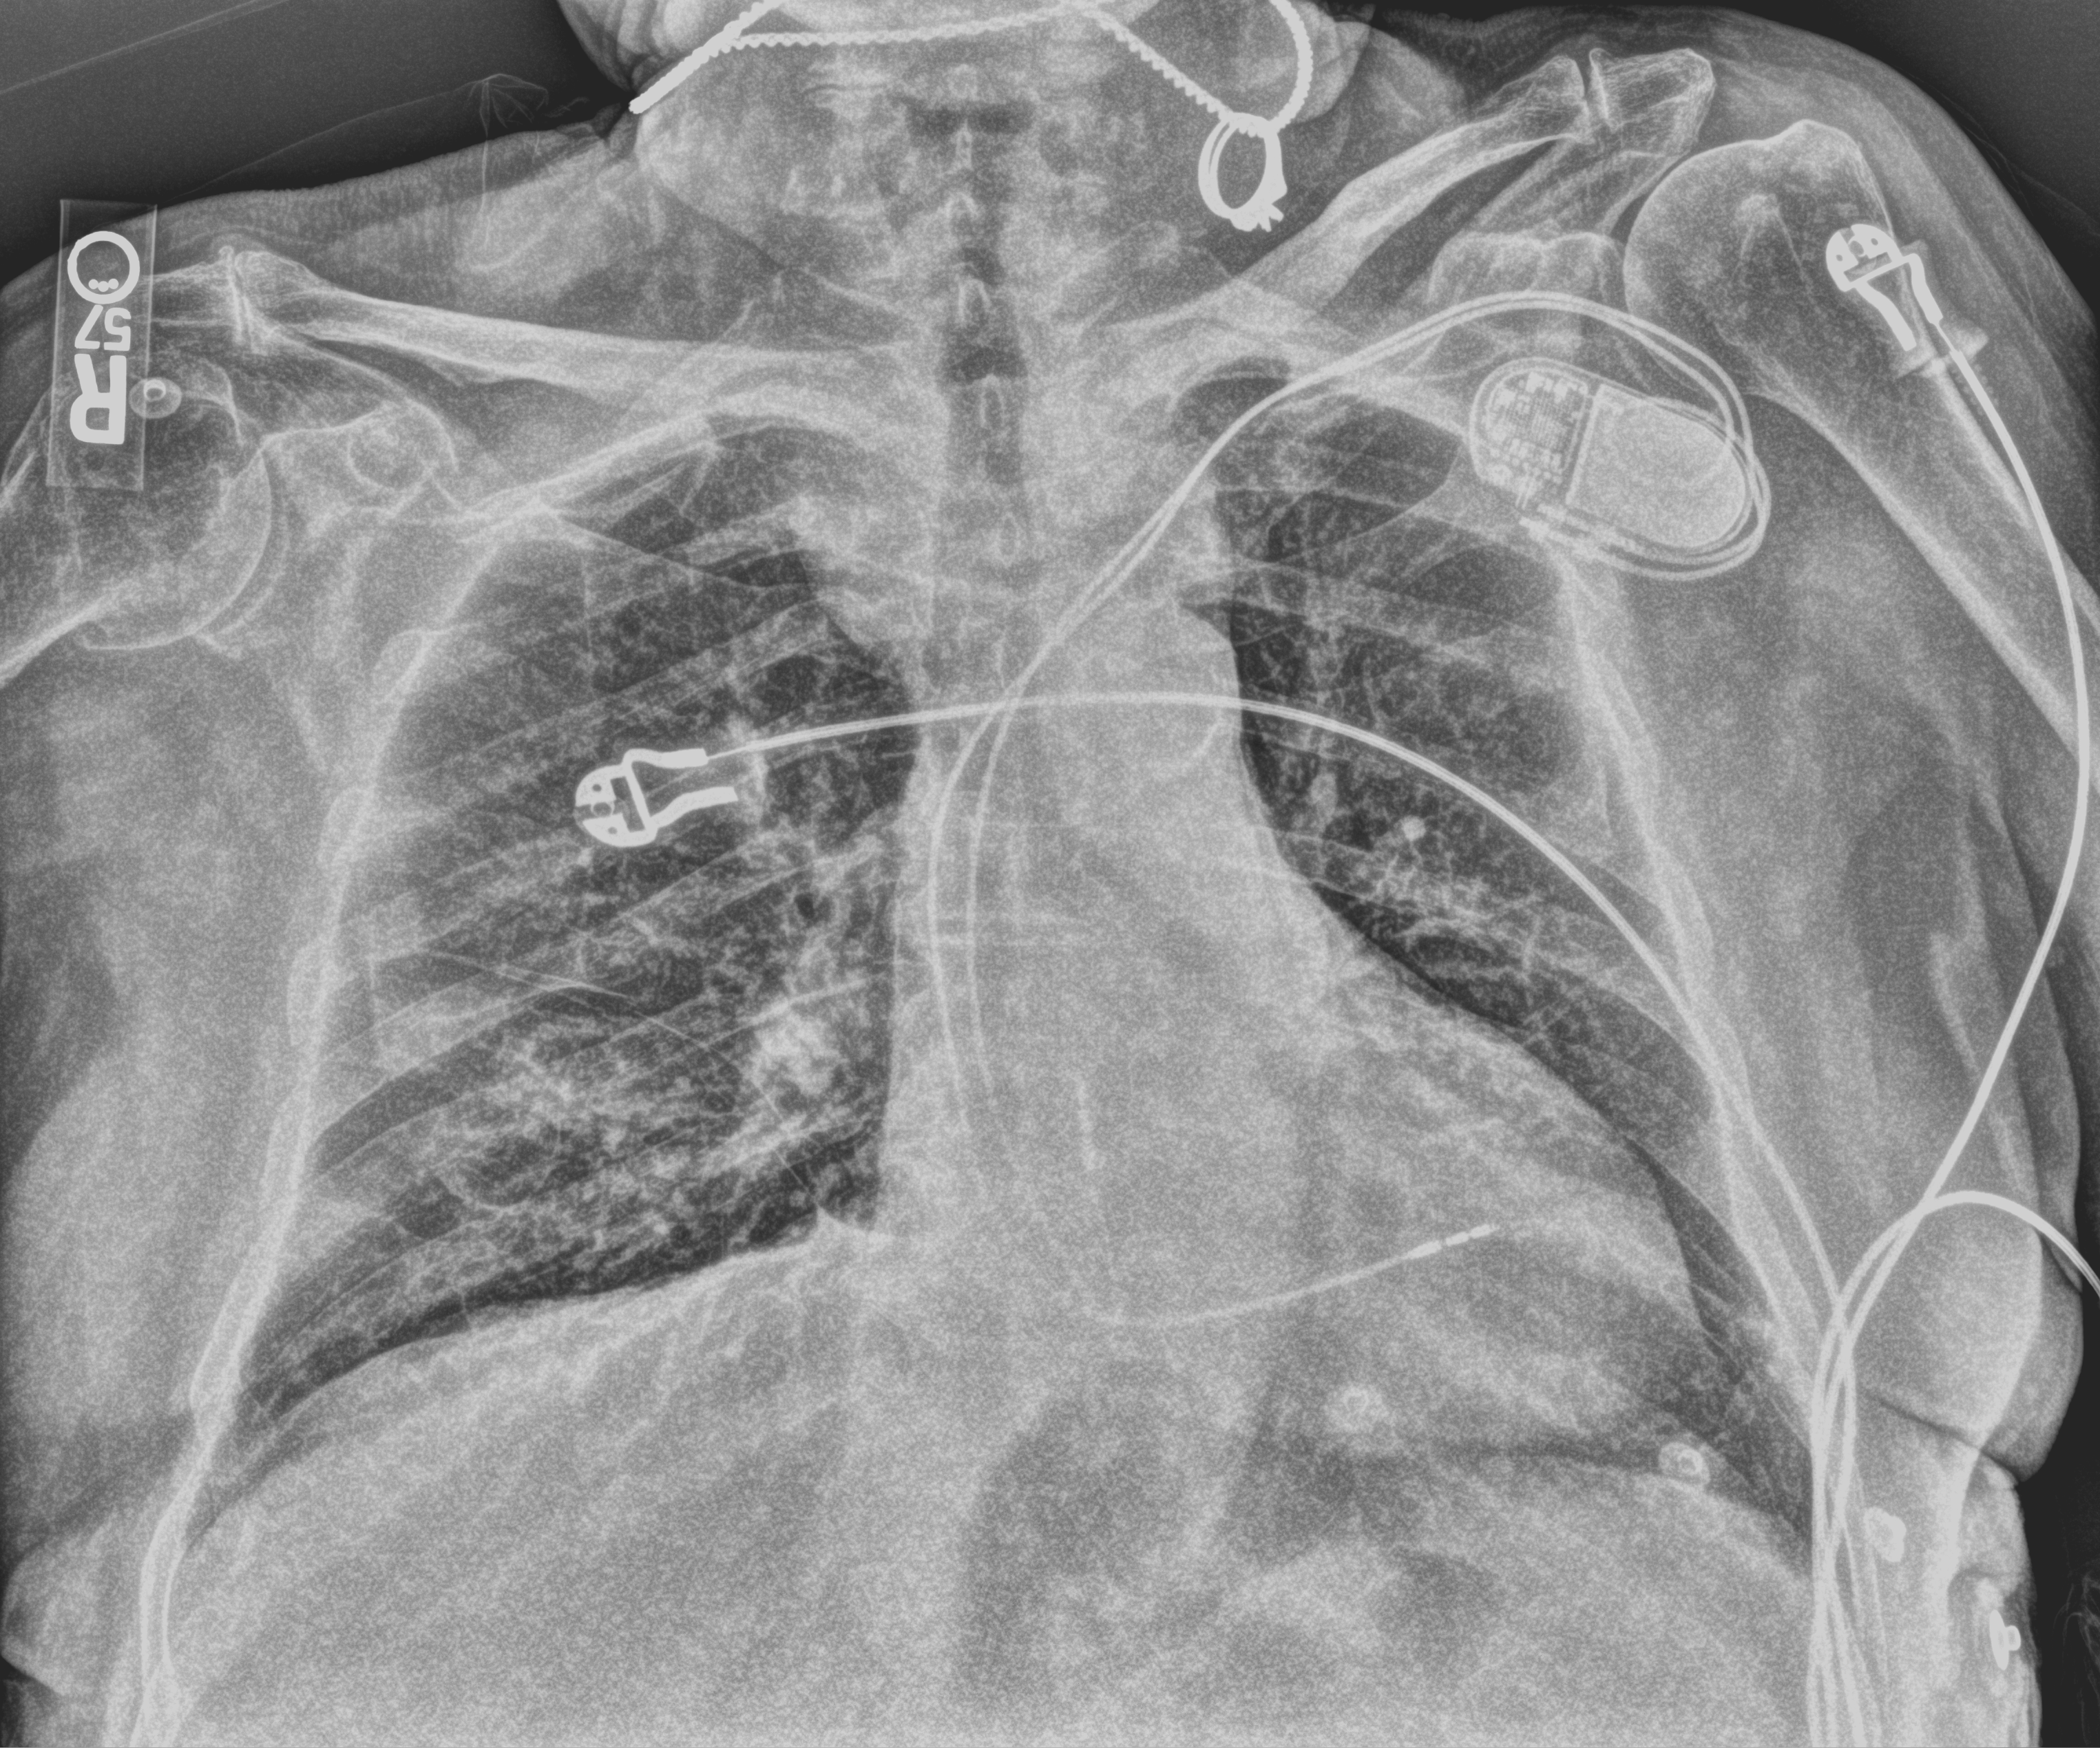
Bedside chest radiograph (computed radiography); anteroposterior (AP) projection. Male patient hospitalised with COVID-19, age 75–90 years.
From the hospital-stay record, not from the radiograph (when in the stay this image was taken is not recorded):
- mechanically ventilated during this hospital stay: no
- admitted to intensive care during this hospital stay: no